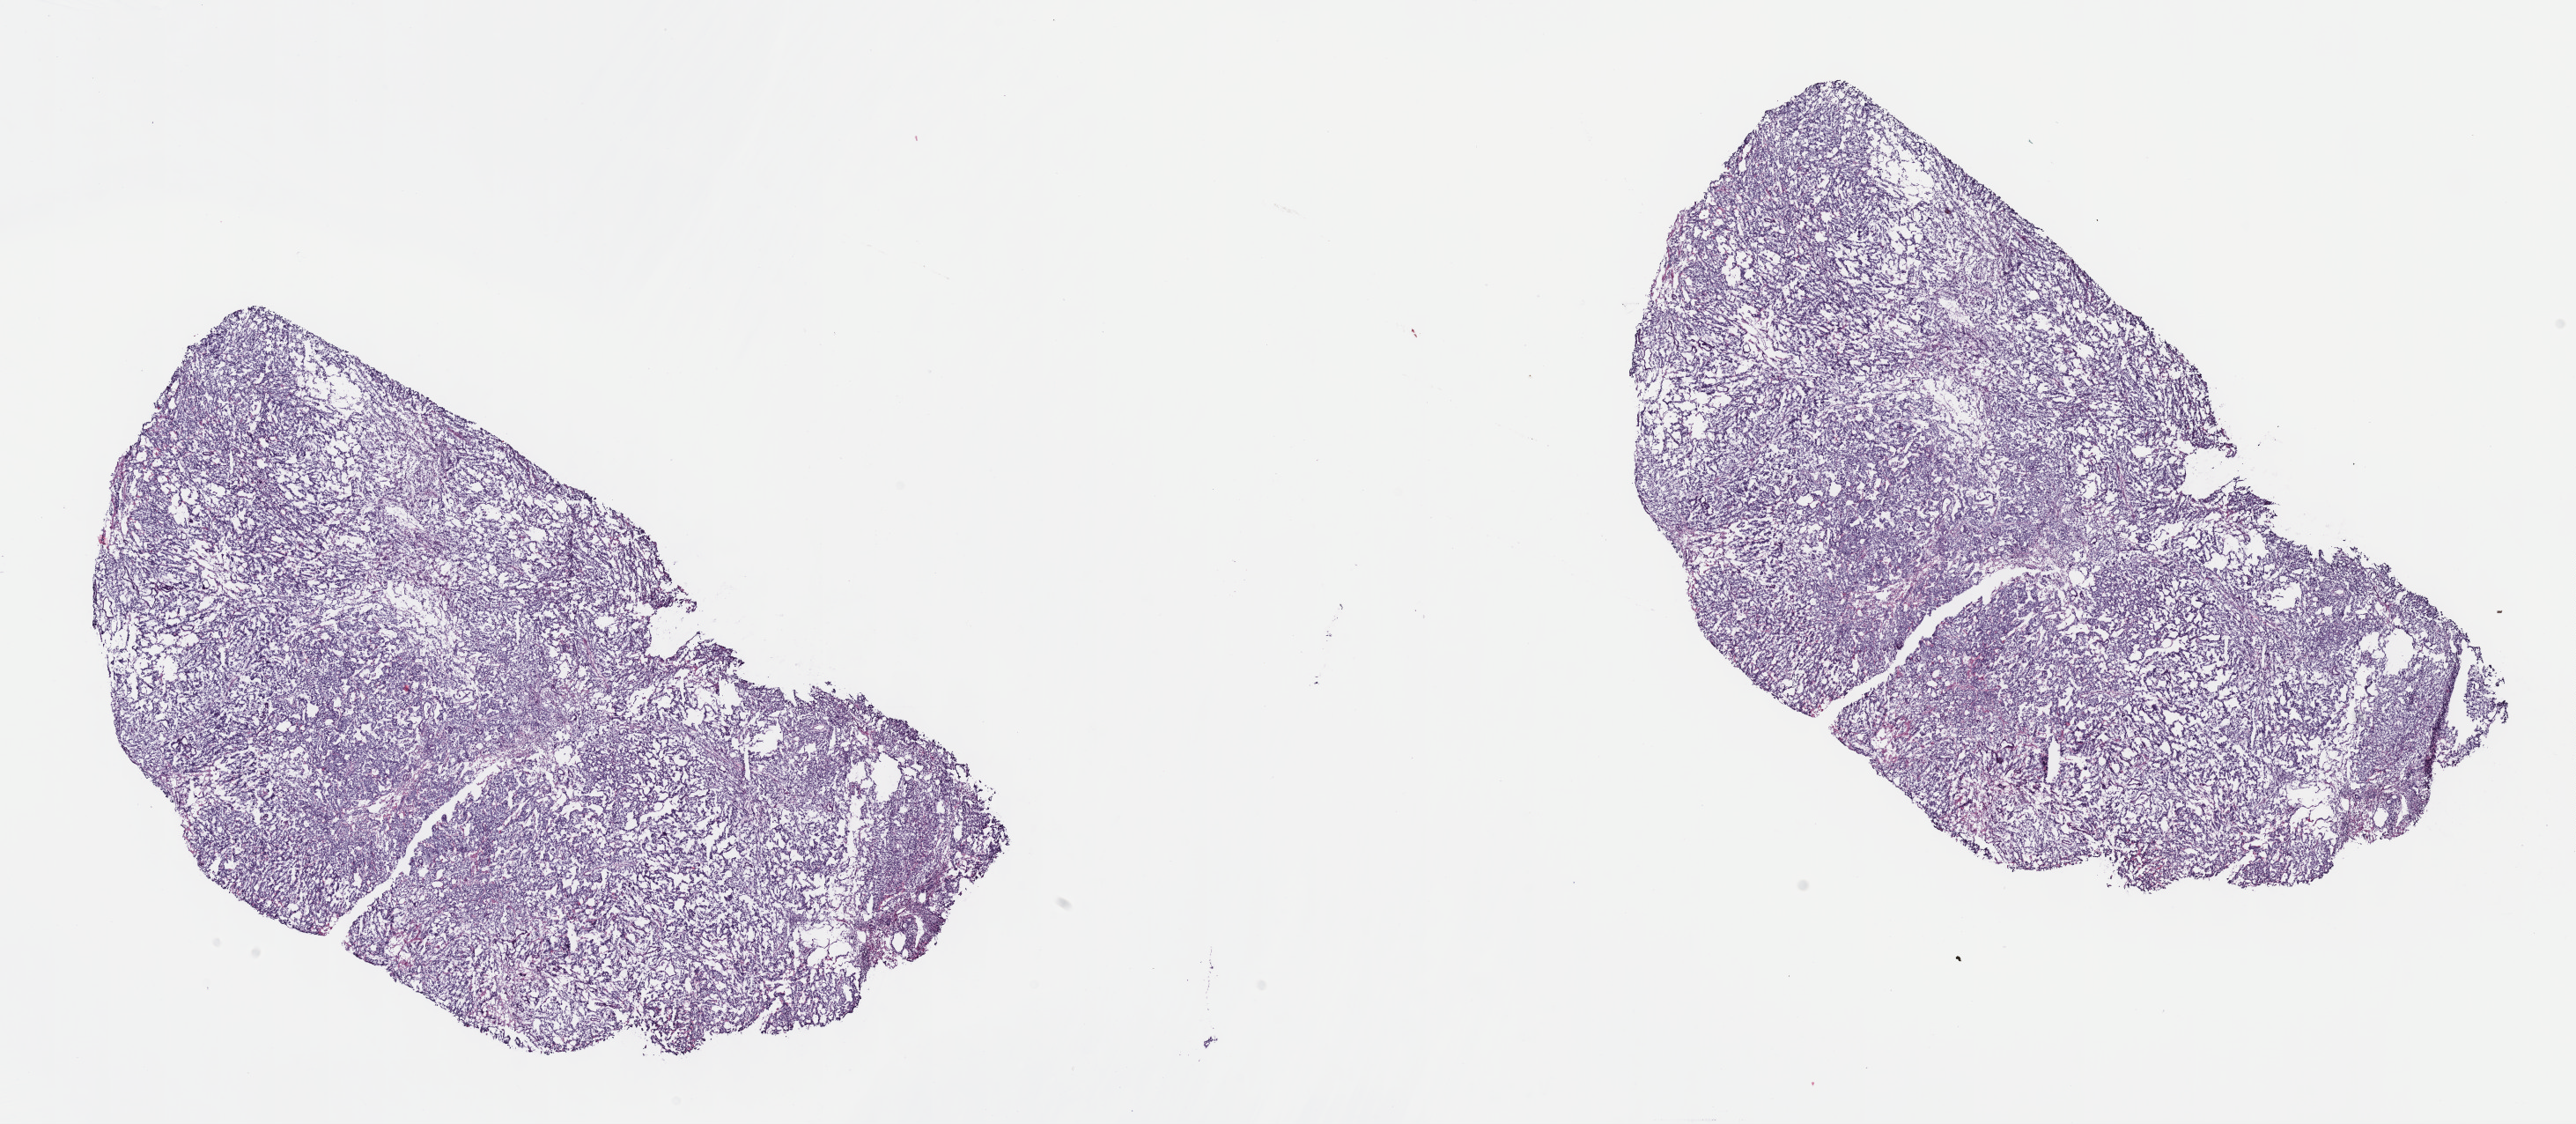
Digitized Hematoxylin and eosin (H&E) stained tissue section (whole slide), whole scanned area (about 23.7 x 10.3 mm, acquisition: 40x scan) shown as a low-resolution overview, frozen section from the top of the tissue portion, testis, primary tumour sample. Male, age 31 years at initial diagnosis. Pathologist review of this section (percent, as recorded): tumour cells 85%, tumour nuclei 90%, normal cells 0%, stromal cells 15%, necrosis 0%. Inflammatory infiltration, as recorded: lymphocyte infiltration 0%, monocyte infiltration 0%, neutrophil infiltration 0%.
TNM: T1 N0 M0. Laterality: left. AJCC pathologic stage: IS. Pathologic diagnosis: Yolk sac tumor.